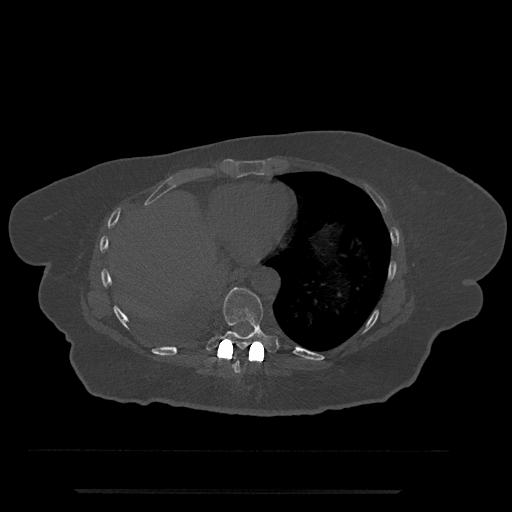
CT including the spine, one axial slice. Reconstruction kernel Br40s/3. 120 kVp. Bone window (W 1800 / L 400 HU). 512 × 512 image matrix. Female patient, age 51 years. From the clinical record (not read from this slice): primary cancer: neuro.
Structures marked on this image (semi-automatically segmented with operator editing):
- T8 vertebra: bounding box <234,354,241,374> (left, top, right, bottom; pixels)
- T9 vertebra: <206,287,277,353>